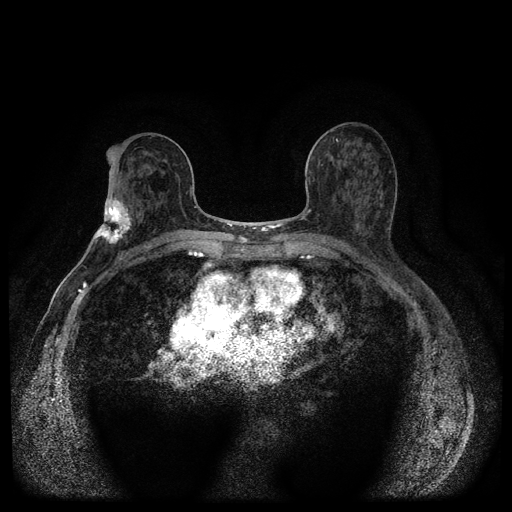
Breast MRI (dynamic contrast-enhanced, multi-phase), one axial slice; position 56 of 116 along the scan axis; dynamic contrast-enhanced series, time point 2 of 5 at this slice position (early post-contrast); 1.5 T; TE 2.7 ms, TR 5.4 ms; 2 mm slice thickness; 512 × 512 image matrix, field of view 340 × 340 mm. Female patient, age 75 years.
Annotated regions visible in this slice (semi-automatically segmented with operator editing):
- breast lesion (labelled 'tumour' in the annotation; benign lesions carry a separate 'benign' label): box from (x=91, y=195) to (x=133, y=247) px